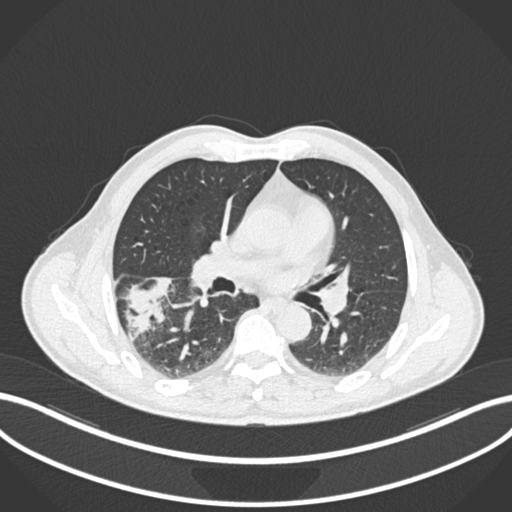
Chest CT, one axial slice. Position 106 of 208 along the scan axis. Reconstruction kernel B30f. Lung window (W 1500 / L -600 HU). 1 mm slice thickness. 512 × 512 image matrix. Patient: male, 58 years. From the clinical record (not read from this slice): clinical TNM (as recorded): T3 N0 M0; histopathological grade: G2.
Outlined on this slice (bounding box drawn by a radiologist):
- lung tumour (recorded histology: squamous cell carcinoma): bounding box <119,264,174,341> (left, top, right, bottom; pixels)